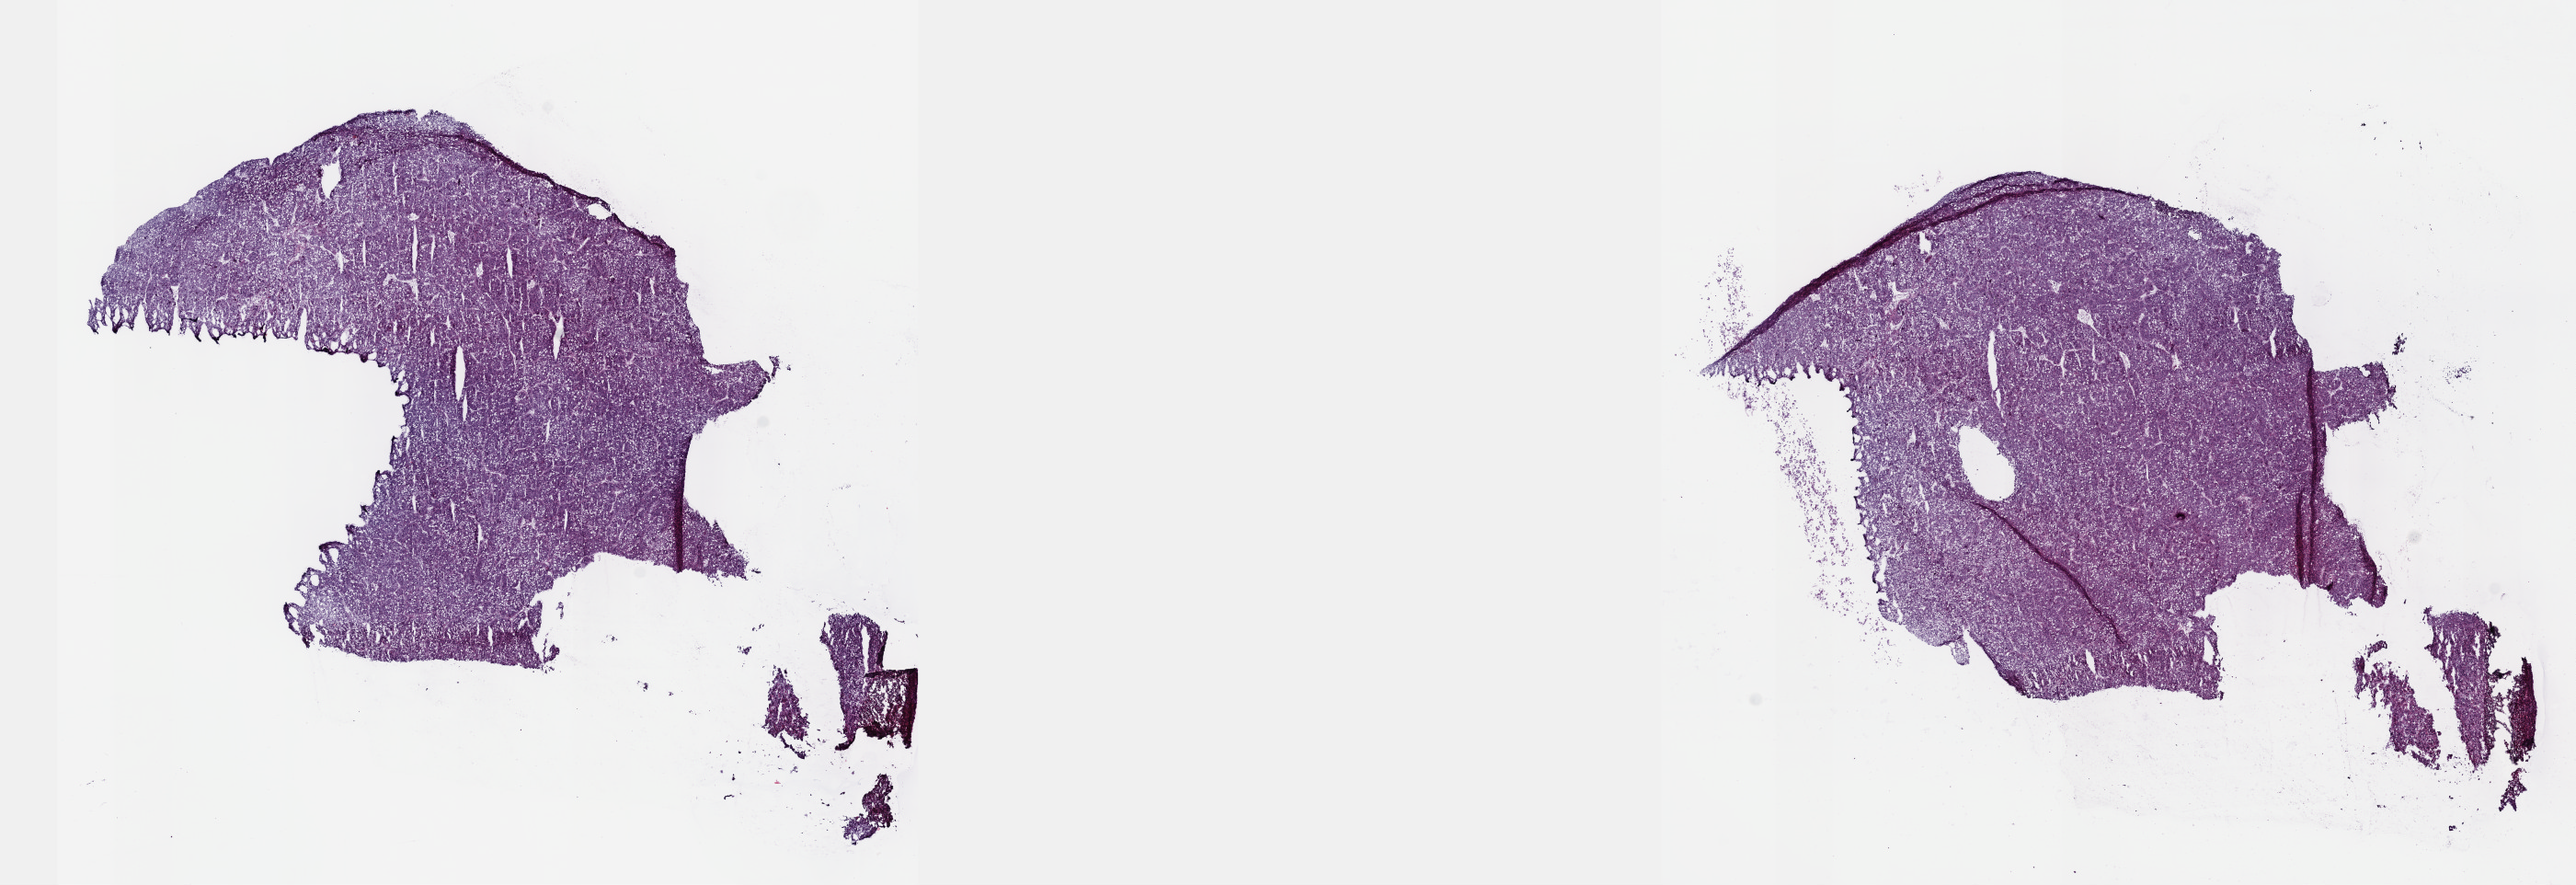
Digitized H&E tissue section (whole slide) — whole scanned area (about 22.6 x 7.8 mm) shown as a low-resolution overview, frozen section from the top of the tissue portion, primary tumour sample from the liver. Patient: male, age at initial diagnosis 57 years. Histologic grade: G2 (moderately differentiated). Composition of this section per pathologist review: tumour cells 94%, tumour nuclei 96%, normal cells 0%, stromal cells 4%, necrosis 2%. Inflammatory infiltration, as recorded: lymphocyte infiltration 2%, monocyte infiltration 0%, neutrophil infiltration 0%.
- histologic diagnosis: Hepatocellular carcinoma, NOS
- TNM: T2 N0 M0
- AJCC pathologic stage: II